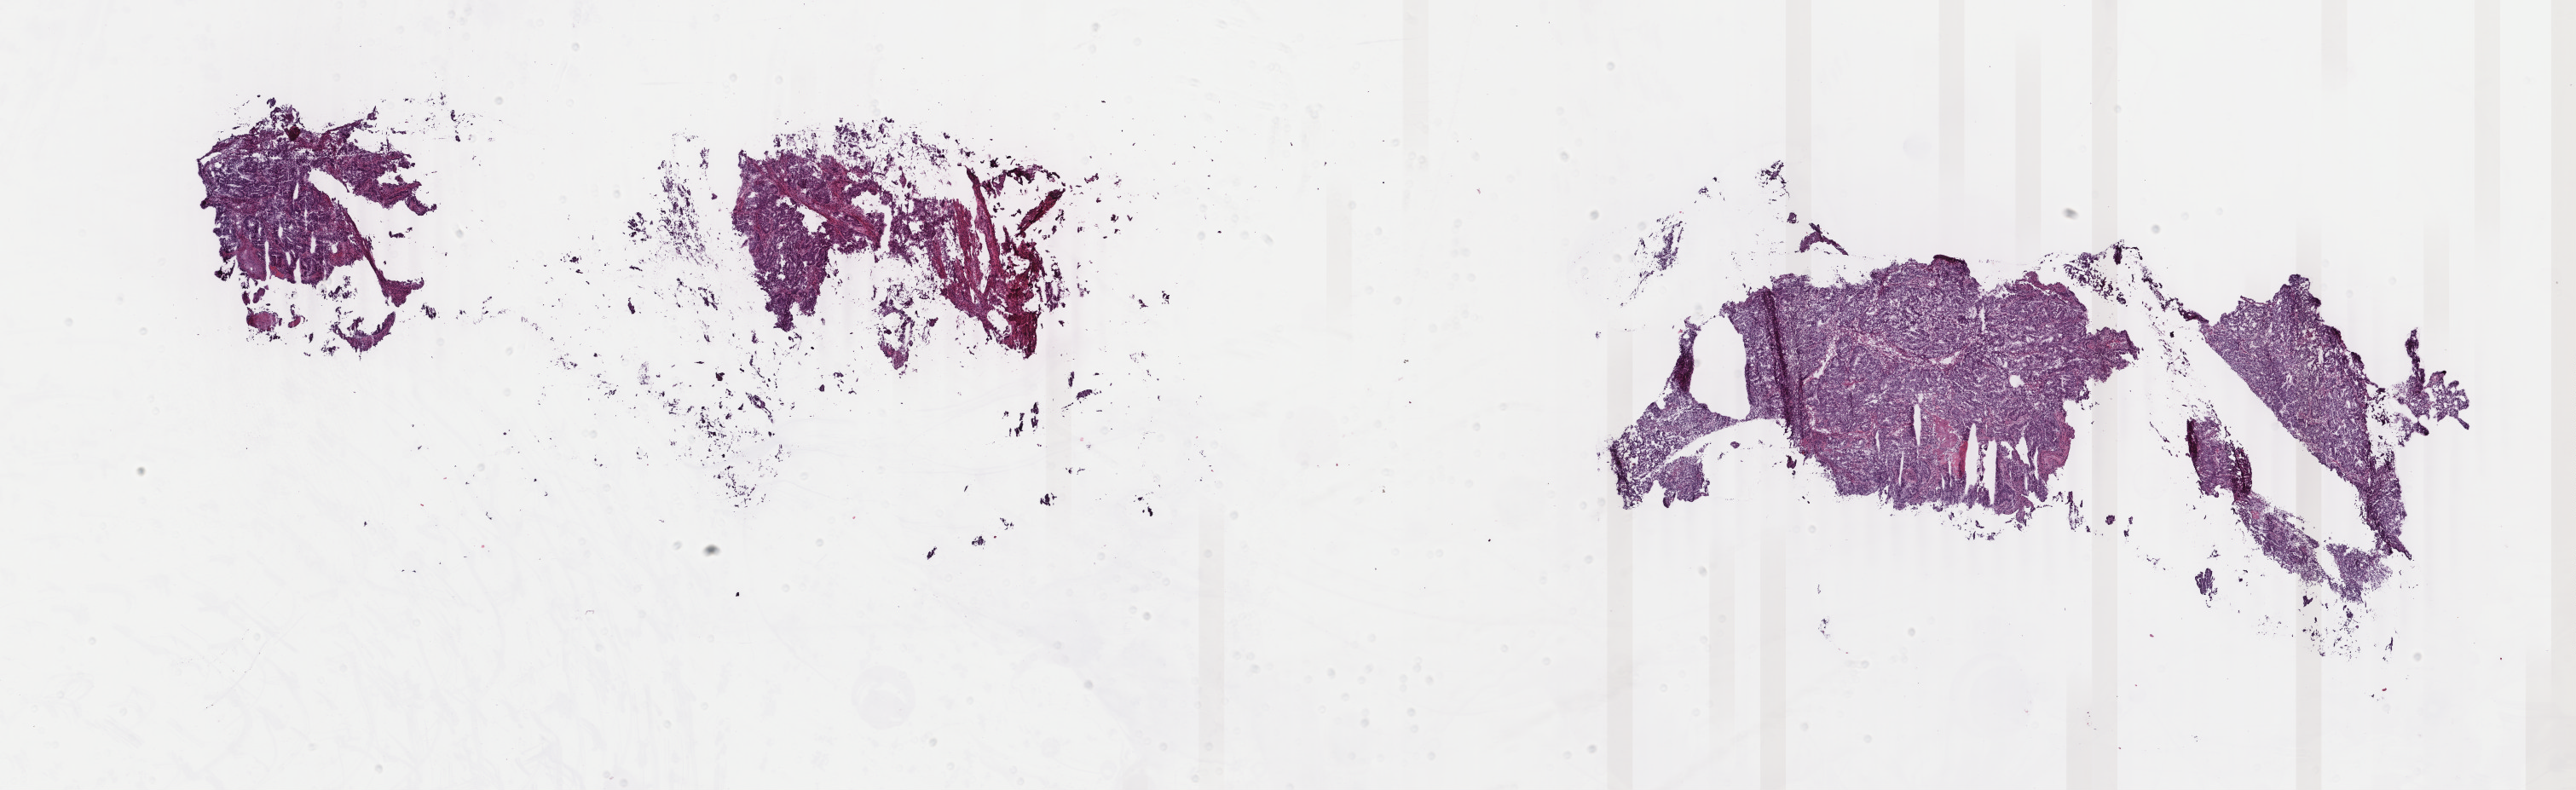
Digitized H&E-stained tissue section (whole slide), a low-resolution overview of the entire scanned area, about 24.0 x 7.4 mm; frozen section from the top of the tissue portion; uterus, primary tumour sample. Patient: female, age at initial diagnosis 52 years. Histologic grade: G2 (moderately differentiated). Pathologist review of this section (percent, as recorded): tumour cells 77%, tumour nuclei 80%, normal cells 10%, stromal cells 10%, necrosis 3%. Inflammatory infiltration, as recorded: lymphocyte infiltration 8%, monocyte infiltration 0%, neutrophil infiltration 1%.
Histologic diagnosis: Endometrioid adenocarcinoma, NOS (endometrium). FIGO stage: IC.